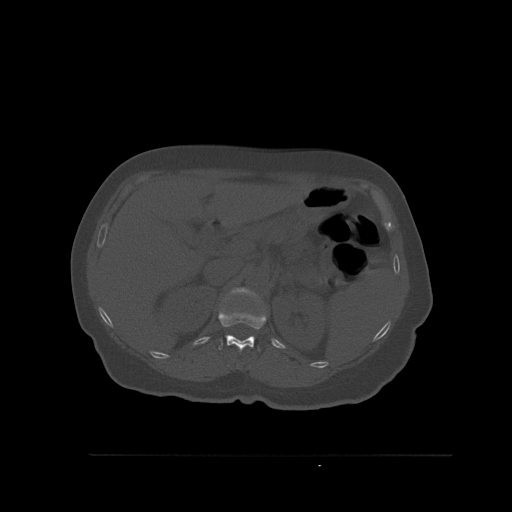
CT including the spine, one axial slice. Position 282 of 527 along the scan axis. Bone window (W 1800 / L 400 HU). 1.5 mm slice thickness. 512 × 512 image matrix, field of view 470 × 470 mm. Patient: female, 73 years. From the clinical record (not read from this slice): primary cancer: breast; vertebrae with lytic lesions (as recorded): L2.
Structures marked on this image (semi-automatically segmented with operator editing):
- L1 vertebra: bounding box <231,287,257,297> (left, top, right, bottom; pixels)
- T12 vertebra: <218,309,267,352>